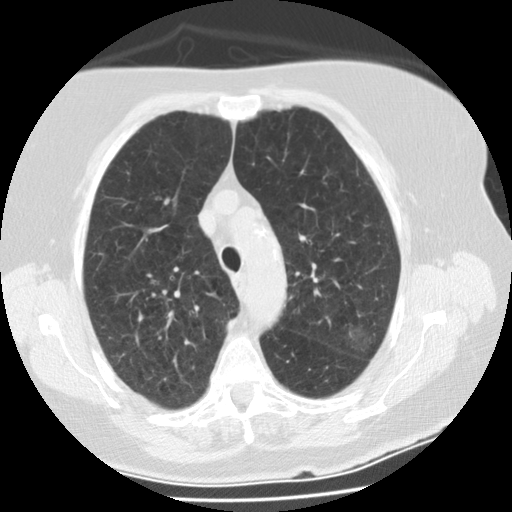
Axial slice from a low-dose chest CT screening exam; second screening round (one year after baseline); lung window (W 1500 / L -600 HU); 2.5 mm slice thickness; standard (soft-tissue) reconstruction kernel (STANDARD); 120 kVp; slice 70 of 297 in the series; 512 × 512 image matrix. Female participant, aged 74 years at enrolment. Former smoker at enrolment.
Lesion marked by an expert reader, bounding box (x1, y1, x2, y2) in pixels: (328, 312, 386, 363). The screening reader recorded 3 non-calcified nodules or masses ≥4 mm on this exam (right lower lobe, left upper lobe, left upper lobe); which of them this box marks is not recorded. Lung cancer was diagnosed 68 days after this screen: bronchiolo-alveolar adenocarcinoma, NOS, left upper lobe, stage IA (AJCC 6th edition), 20 mm at pathology.